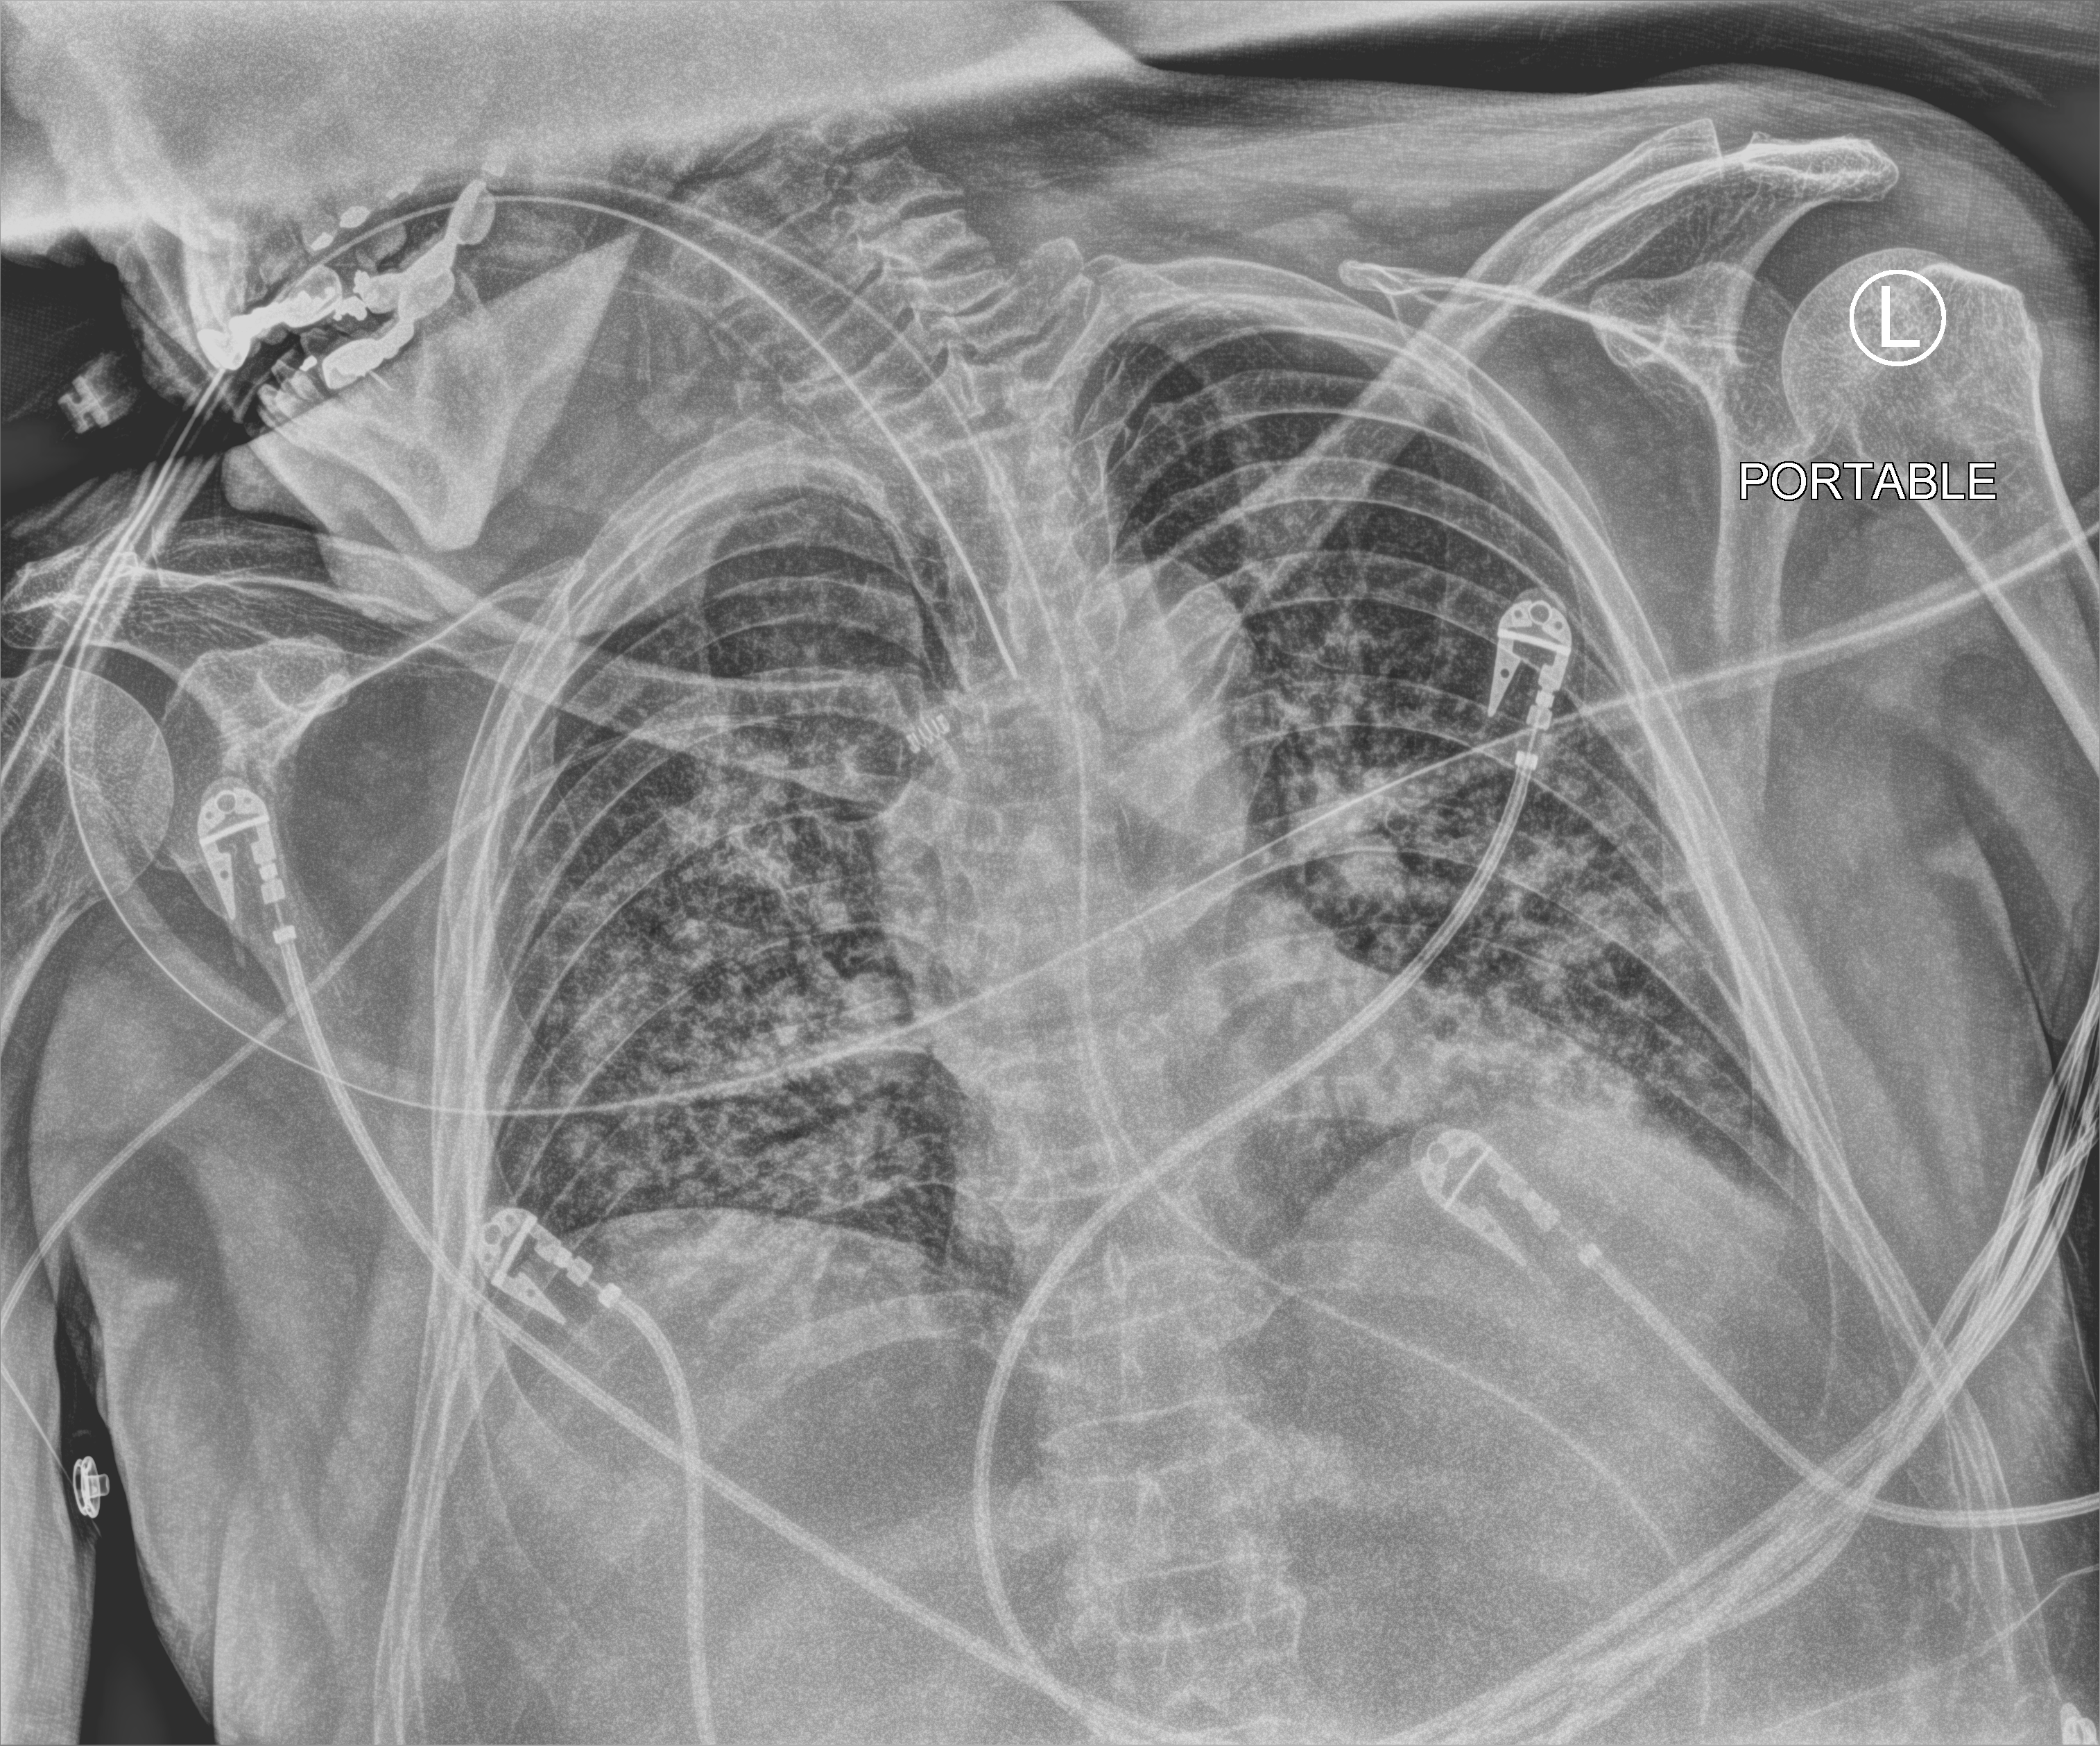
Bedside chest radiograph (computed radiography). Patient hospitalised with COVID-19; male, aged 60–74 years.
Admission-level facts for this patient (not findings on this image; timing relative to this image not recorded):
- length of hospital stay: 19 days
- hypertension (admission record): no